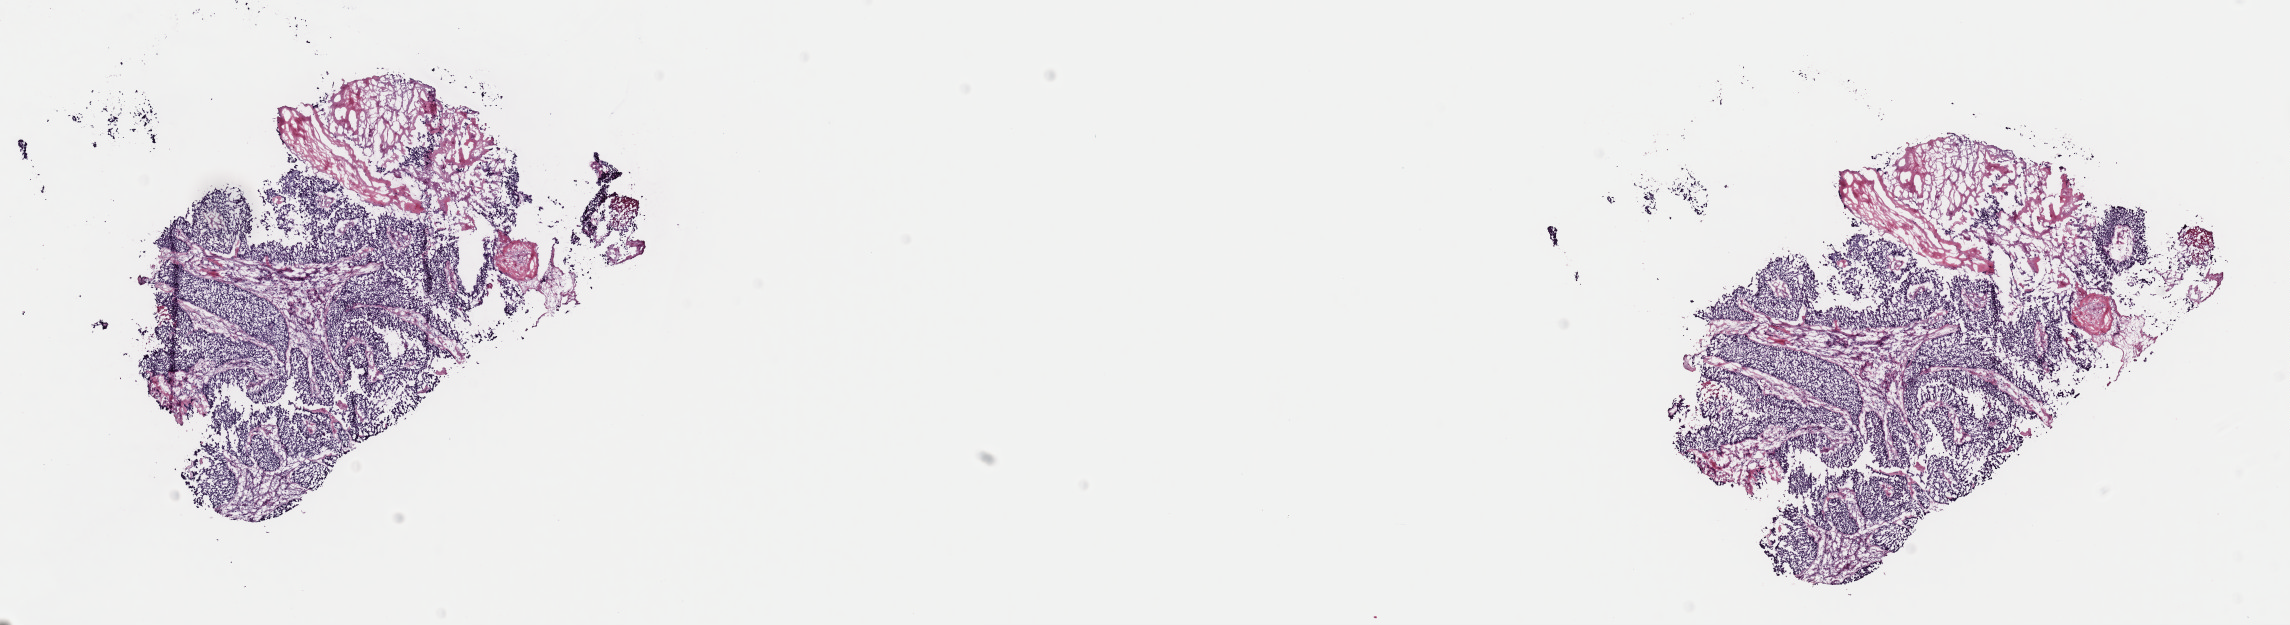
Digitized H&E tissue section (whole slide), shown as a low-resolution overview of the whole scanned area (about 18.1 x 4.9 mm, acquisition: 40x scan). Frozen section from the top of the tissue portion. Primary tumour sample from the bladder. Male patient; age at initial diagnosis 84 years.
Pathologic diagnosis: Transitional cell carcinoma.